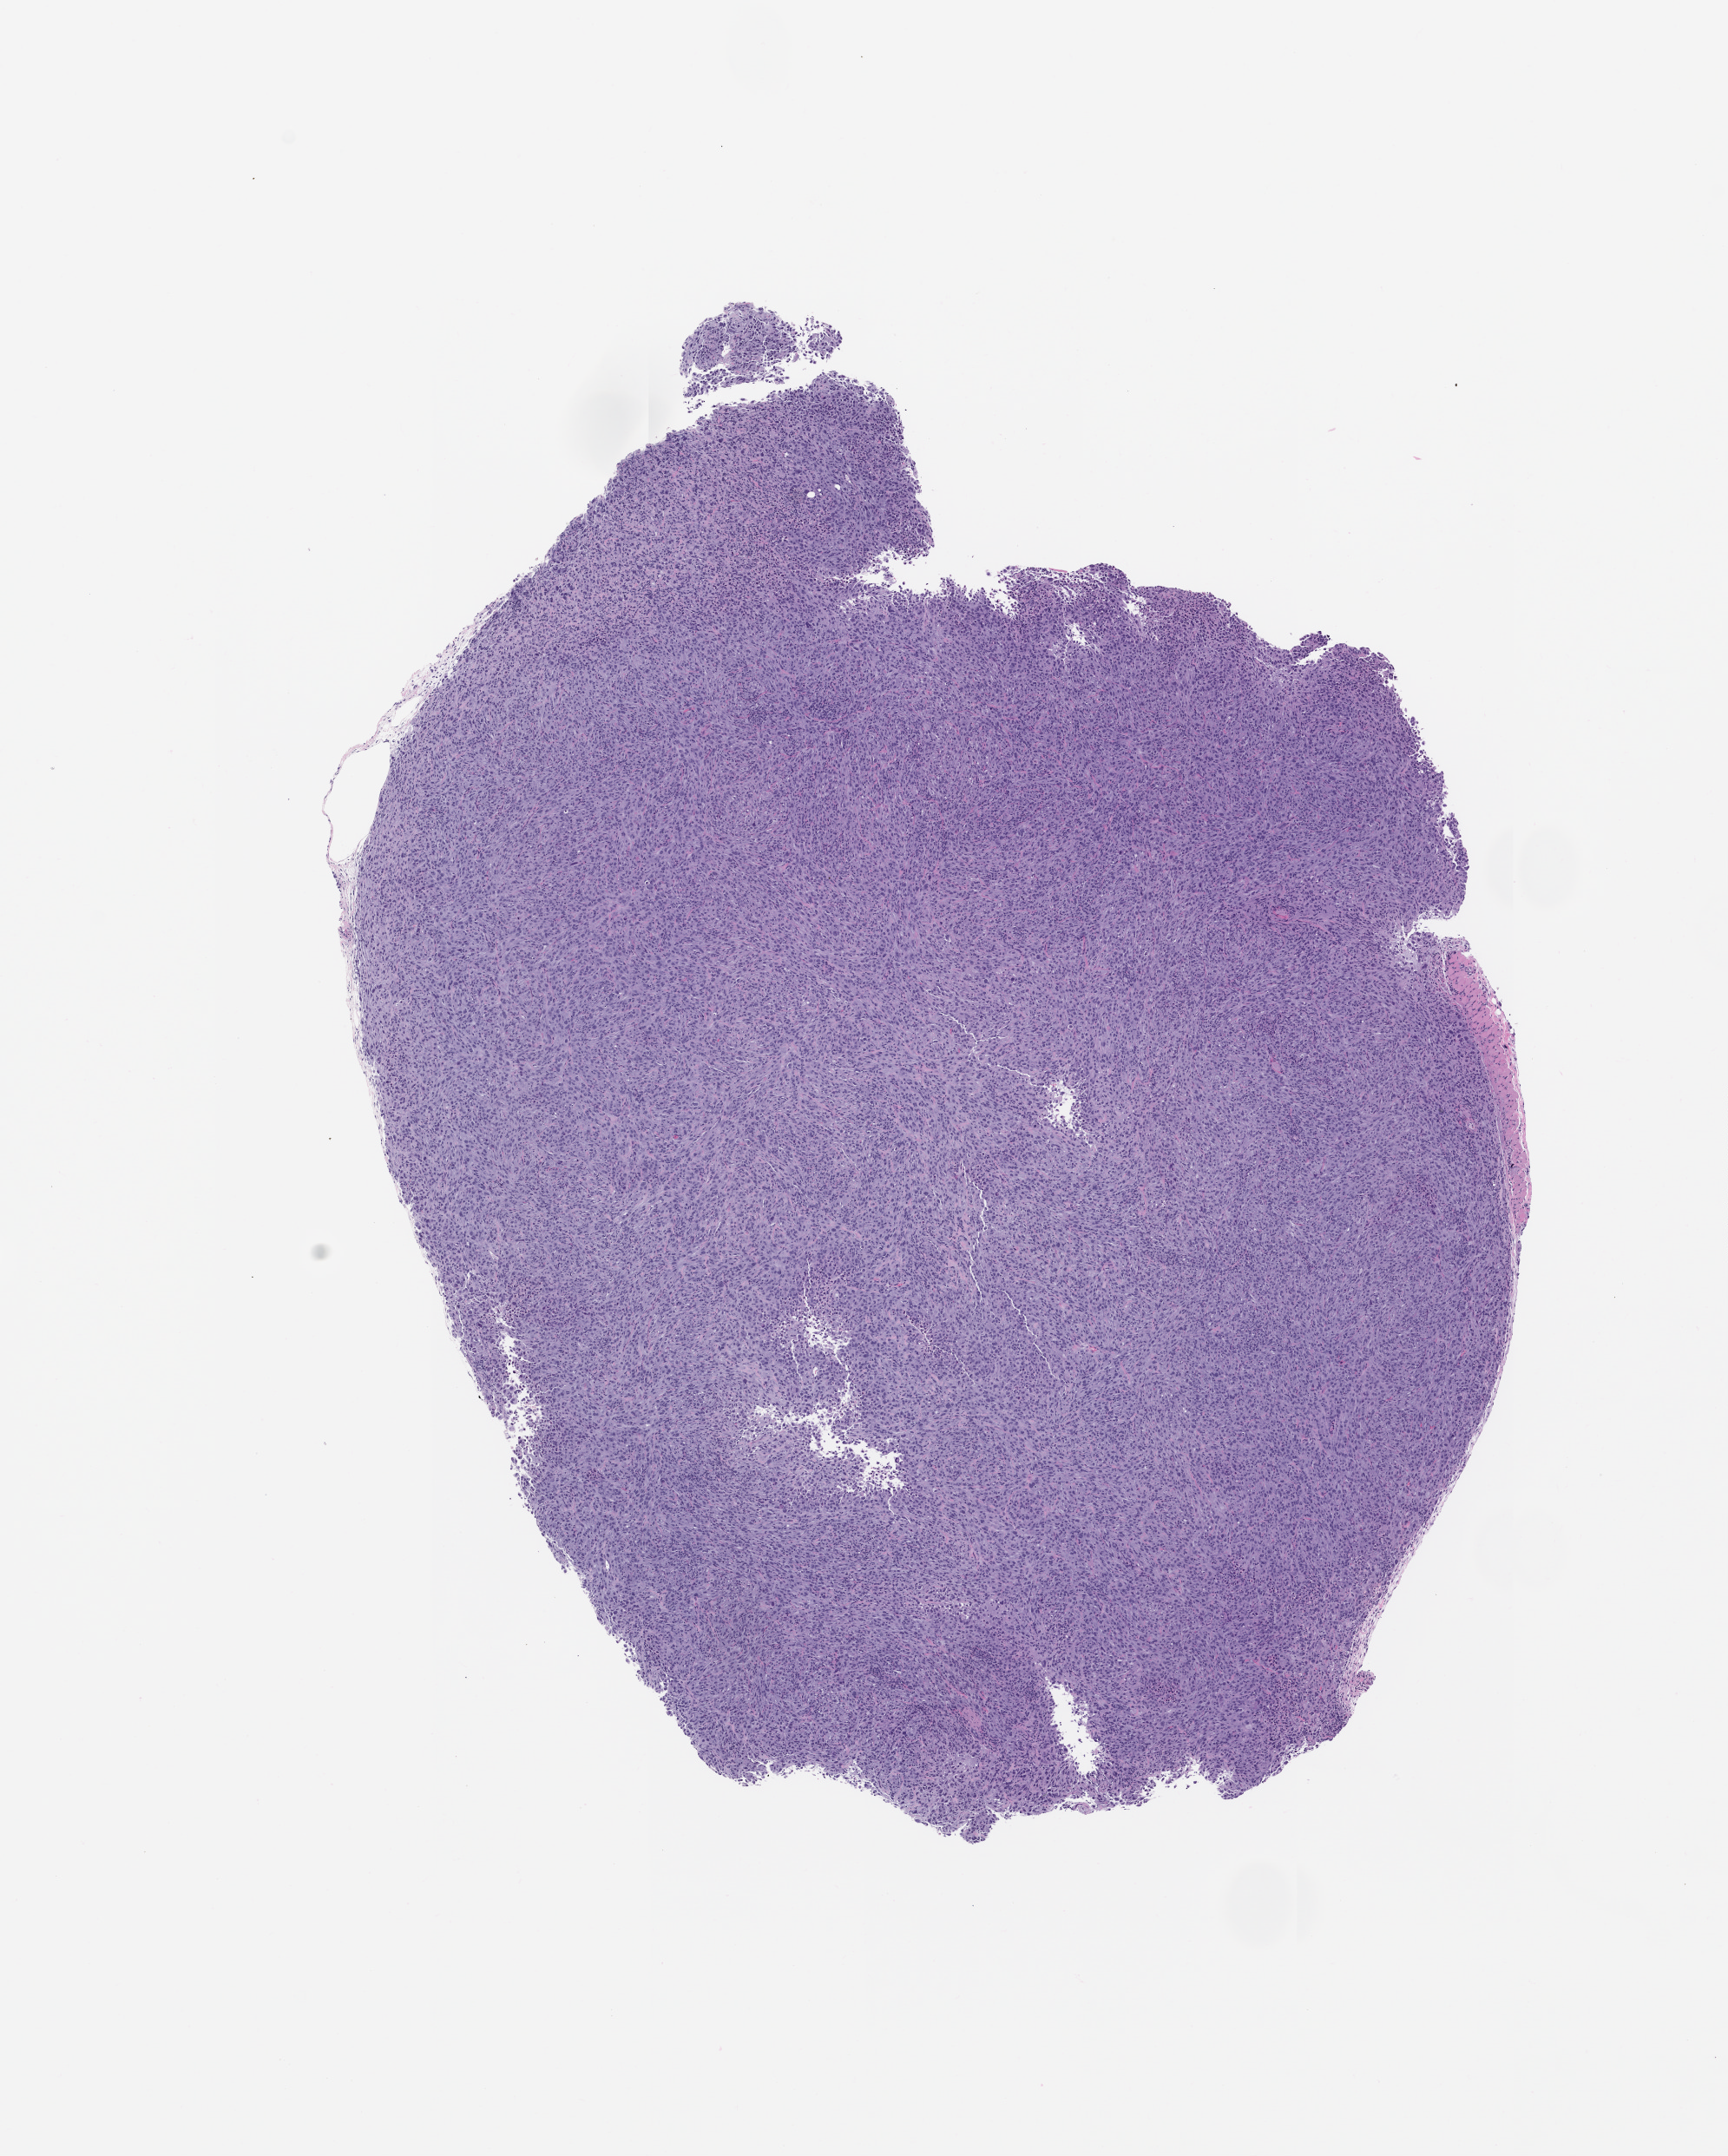
Whole-slide image, H&E: patient-derived xenograft (human tumor grown in a mouse), passage 0 — shown as a low-resolution overview of the whole scanned area (about 8.0 x 10.0 mm), formalin-fixed, paraffin-embedded (FFPE) tissue, tumor site category: thyroid.
Originating patient diagnosis: Thyroid Gland Oncocytic Carcinoma.